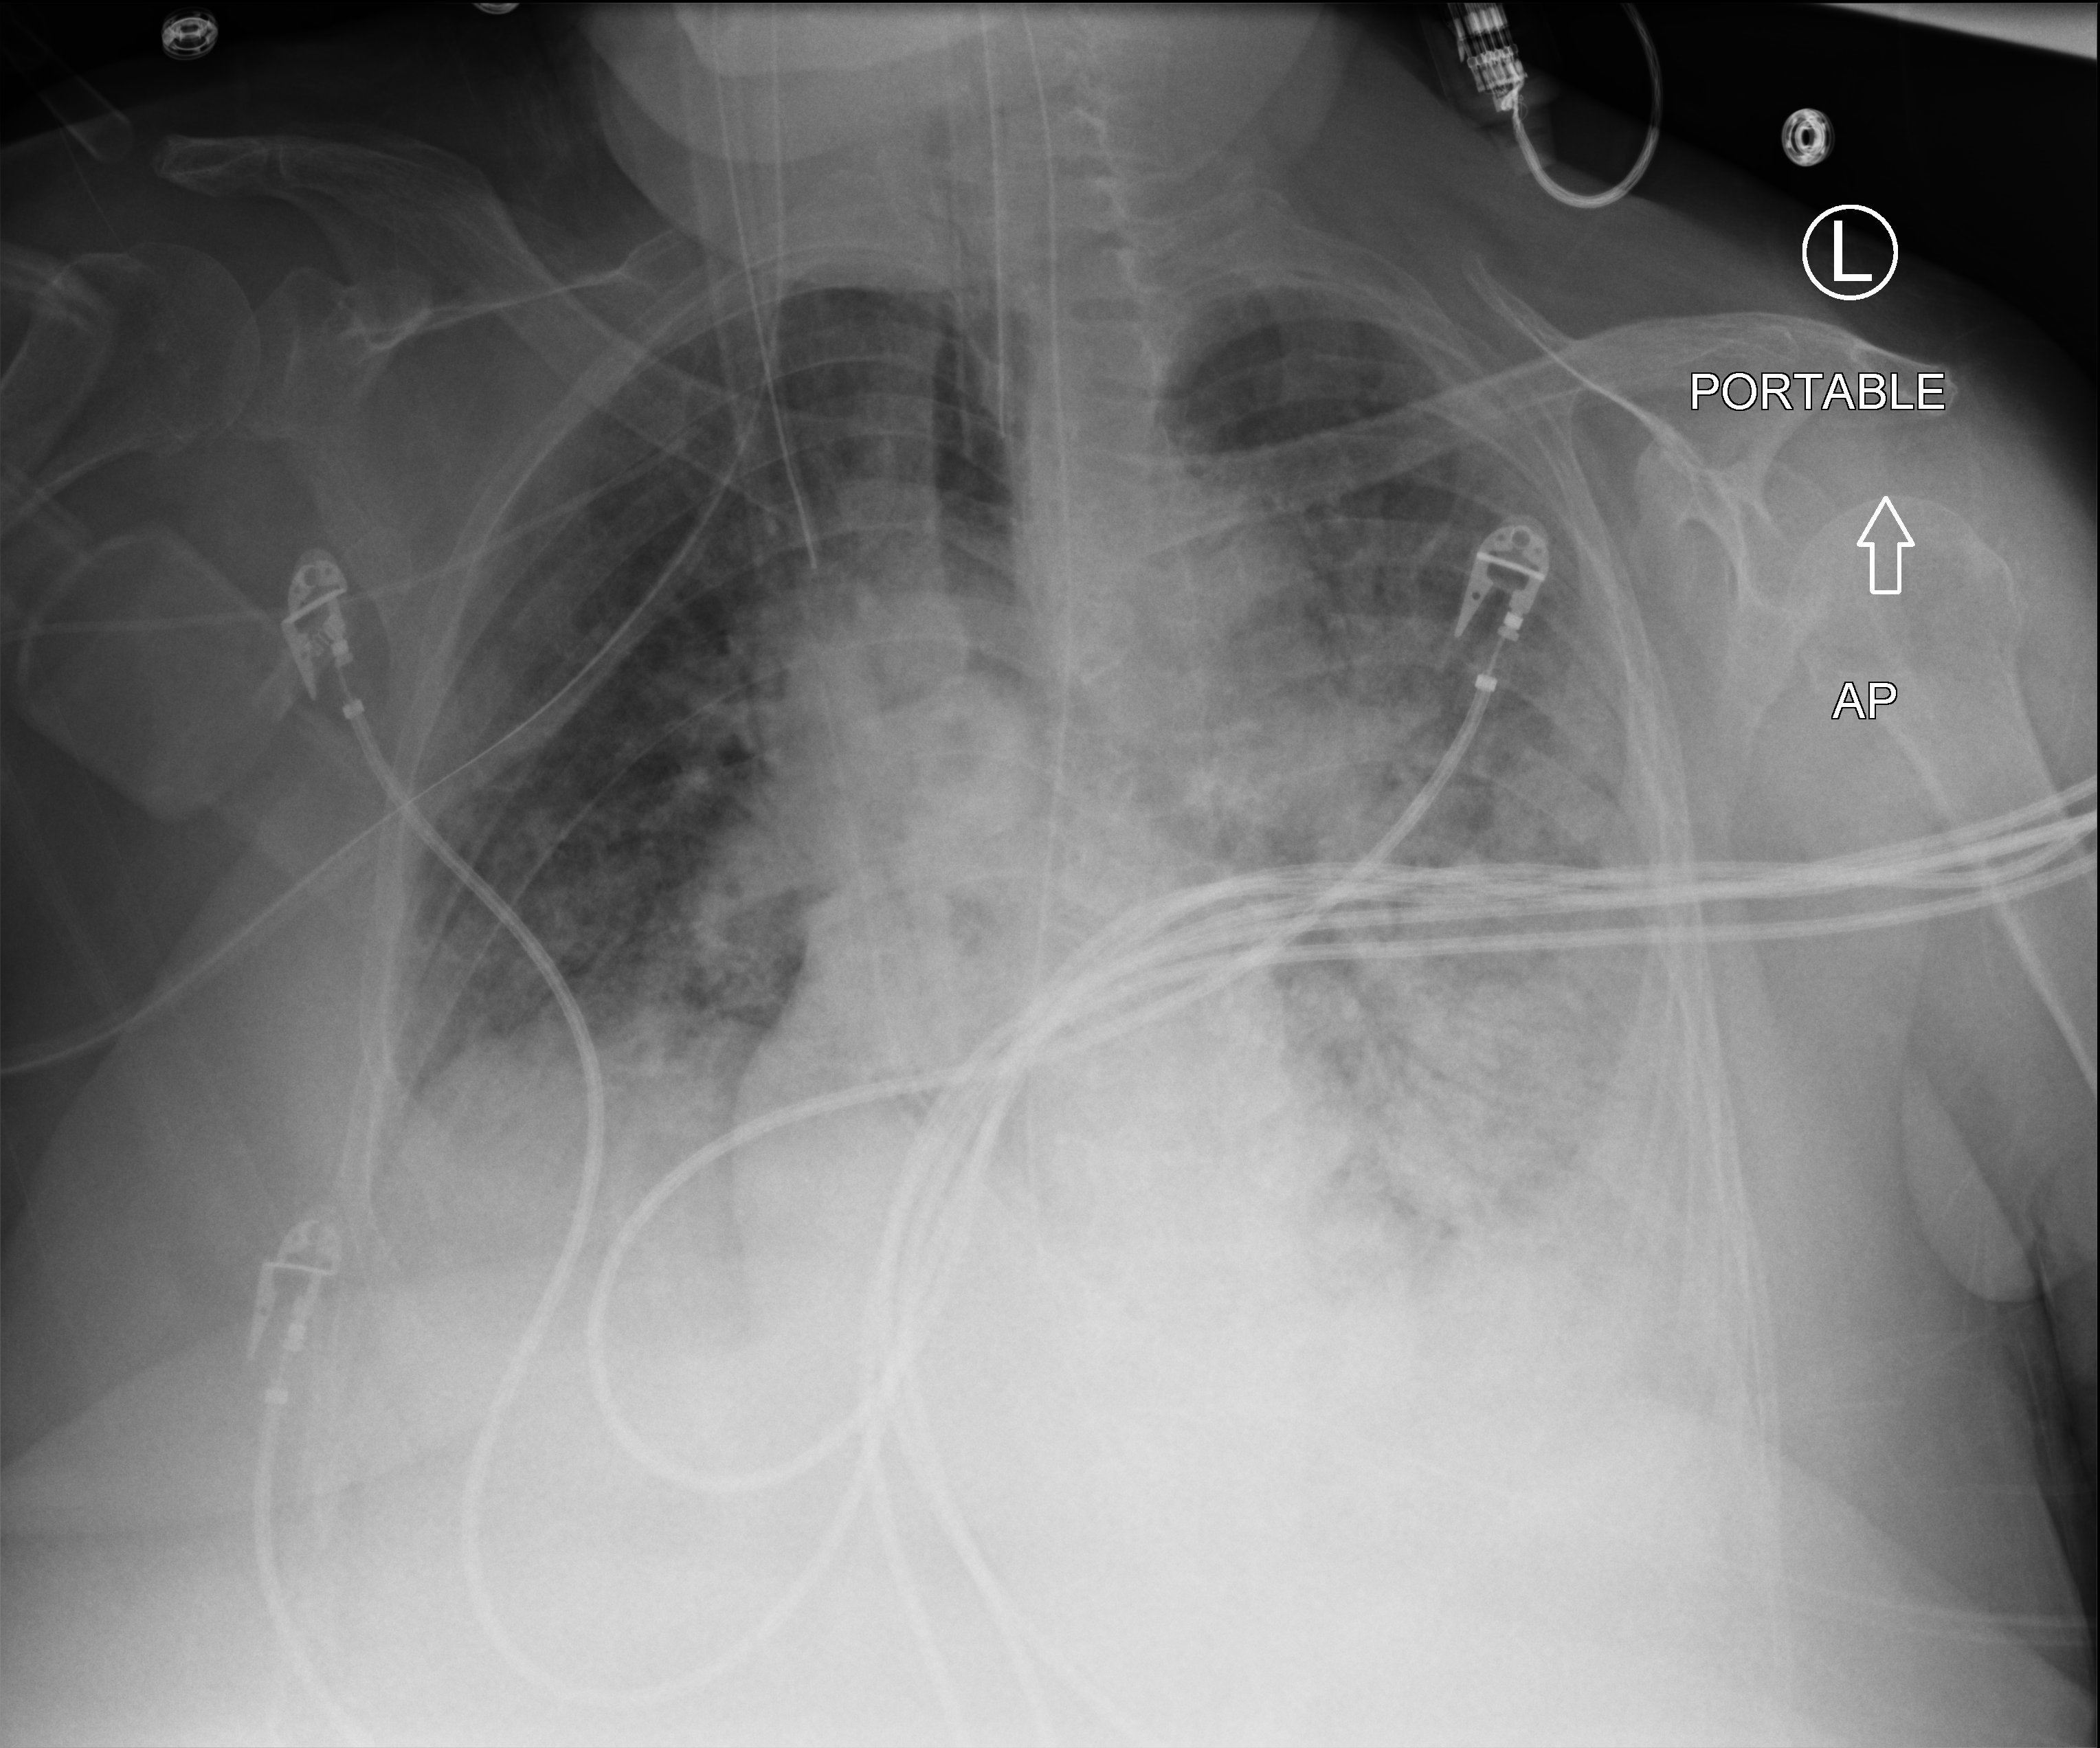
Portable chest radiograph, anteroposterior (AP) projection. Female patient hospitalised with COVID-19, age 60–74 years.
Hospital-stay facts (about this admission, not read from this image; timing relative to this image not recorded):
- other chronic lung disease (admission record): no